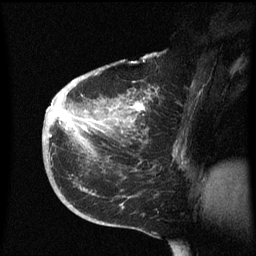
Breast MRI (dynamic contrast-enhanced), one sagittal slice; position 32 of 60 along the scan axis; dynamic contrast-enhanced series, image 2 of 3 at this slice position (ordered by acquisition); 1.5 T; TE 4.2 ms, TR 8.4 ms; 2.3 mm slice thickness; 256 × 256 image matrix, field of view 200 × 200 mm. Female patient, age 38 years. From the clinical record (not read from this slice): setting: breast cancer imaged before/during neoadjuvant chemotherapy; receptor status: HER2-positive.
Outlined on this slice (semi-automatically segmented with operator editing):
- analysis volume of interest (the breast-tissue region the enhancement analysis was run in; not a lesion): box from (x=42, y=78) to (x=182, y=213) px
- tumour enhancement mask (voxels above the 70 % enhancement threshold inside the analysis volume of interest): (x=50, y=102)–(x=145, y=137)